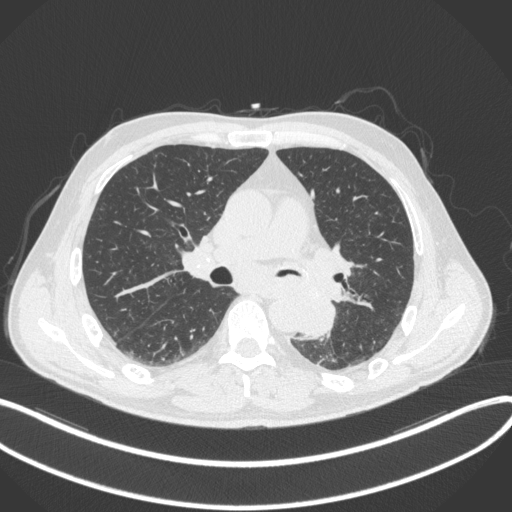
Chest CT, one axial slice. Slice 199 of 328 in the series (ordered by position). Reconstruction kernel B31f. 120 kVp. Lung window (W 1500 / L -600 HU). 1 mm slice thickness. 512 × 512 image matrix. Patient: male, 59 years. Case-level facts recorded for this patient, not image findings: clinical TNM (as recorded): T2a N2 M0.
Annotated regions visible in this slice (bounding box drawn by a radiologist):
- lung tumour (recorded histology: squamous cell carcinoma): bounding box (x1, y1, x2, y2) in pixels: (299, 288, 337, 343)